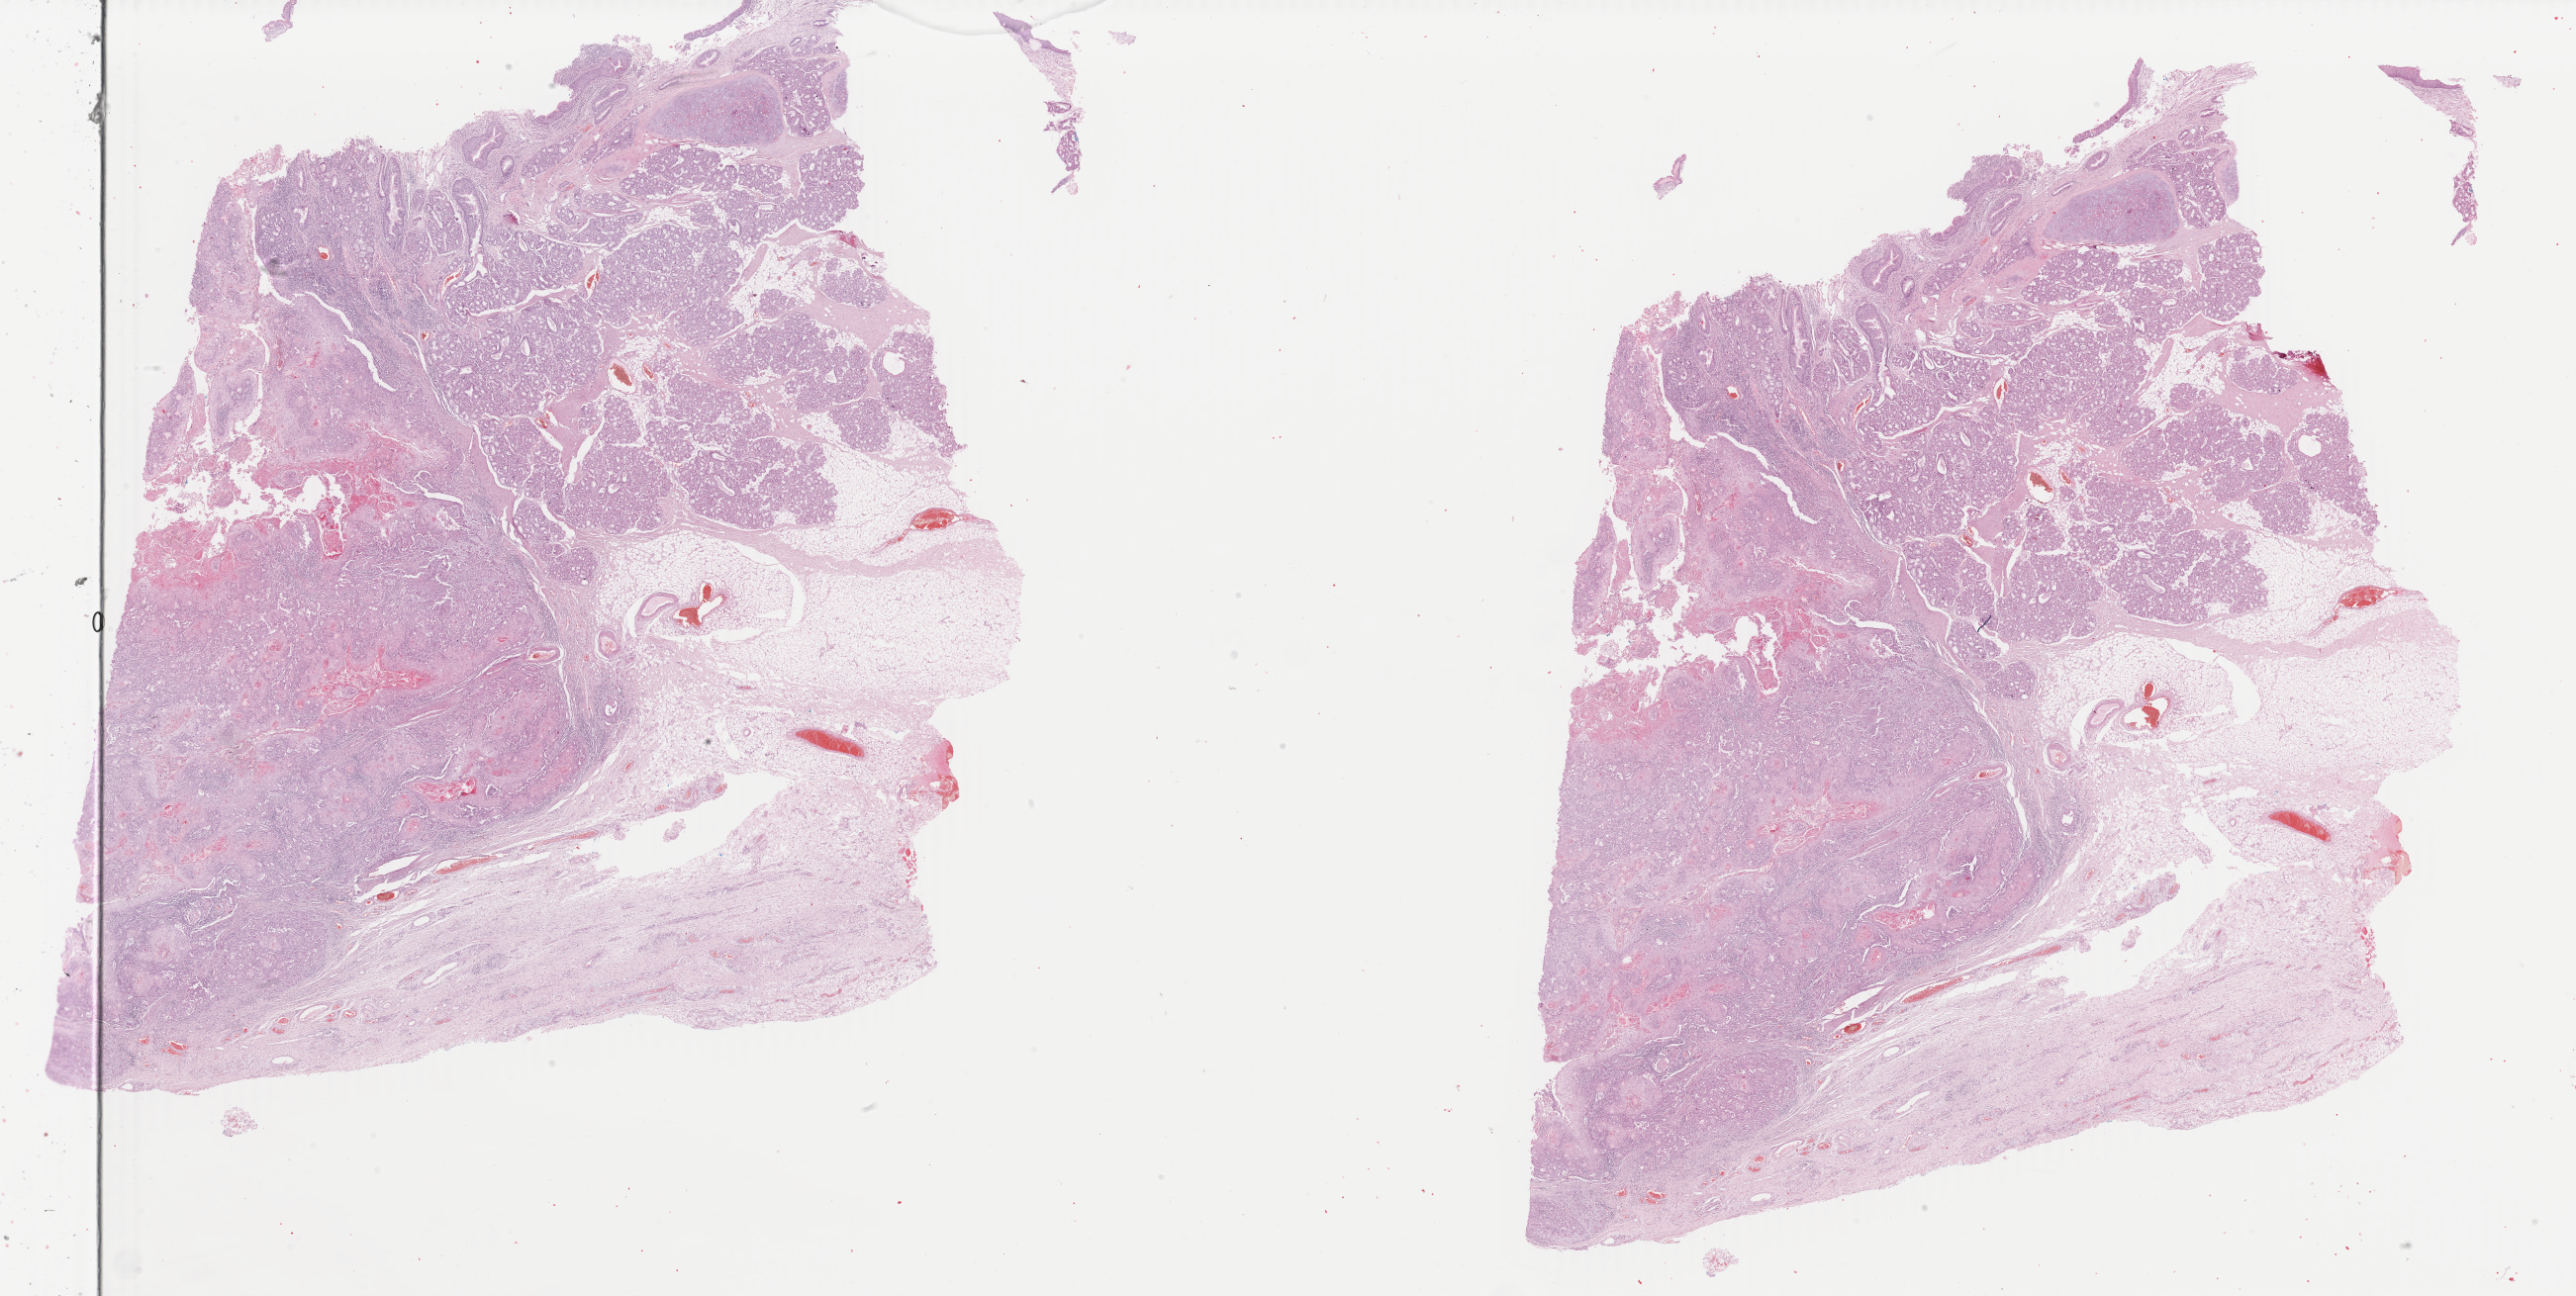
Digitized Hematoxylin and eosin (H&E) stained tissue section (whole slide) — a low-resolution overview of the entire scanned area, about 41.4 x 20.8 mm (from a 40x scan); formalin-fixed paraffin-embedded (FFPE) diagnostic section; primary tumour sample from the head and neck. Patient: male, age at initial diagnosis 61 years. Histologic grade: G2 (moderately differentiated).
- AJCC pathologic stage: IVA
- pathologic diagnosis: Squamous cell carcinoma, NOS (larynx, NOS)